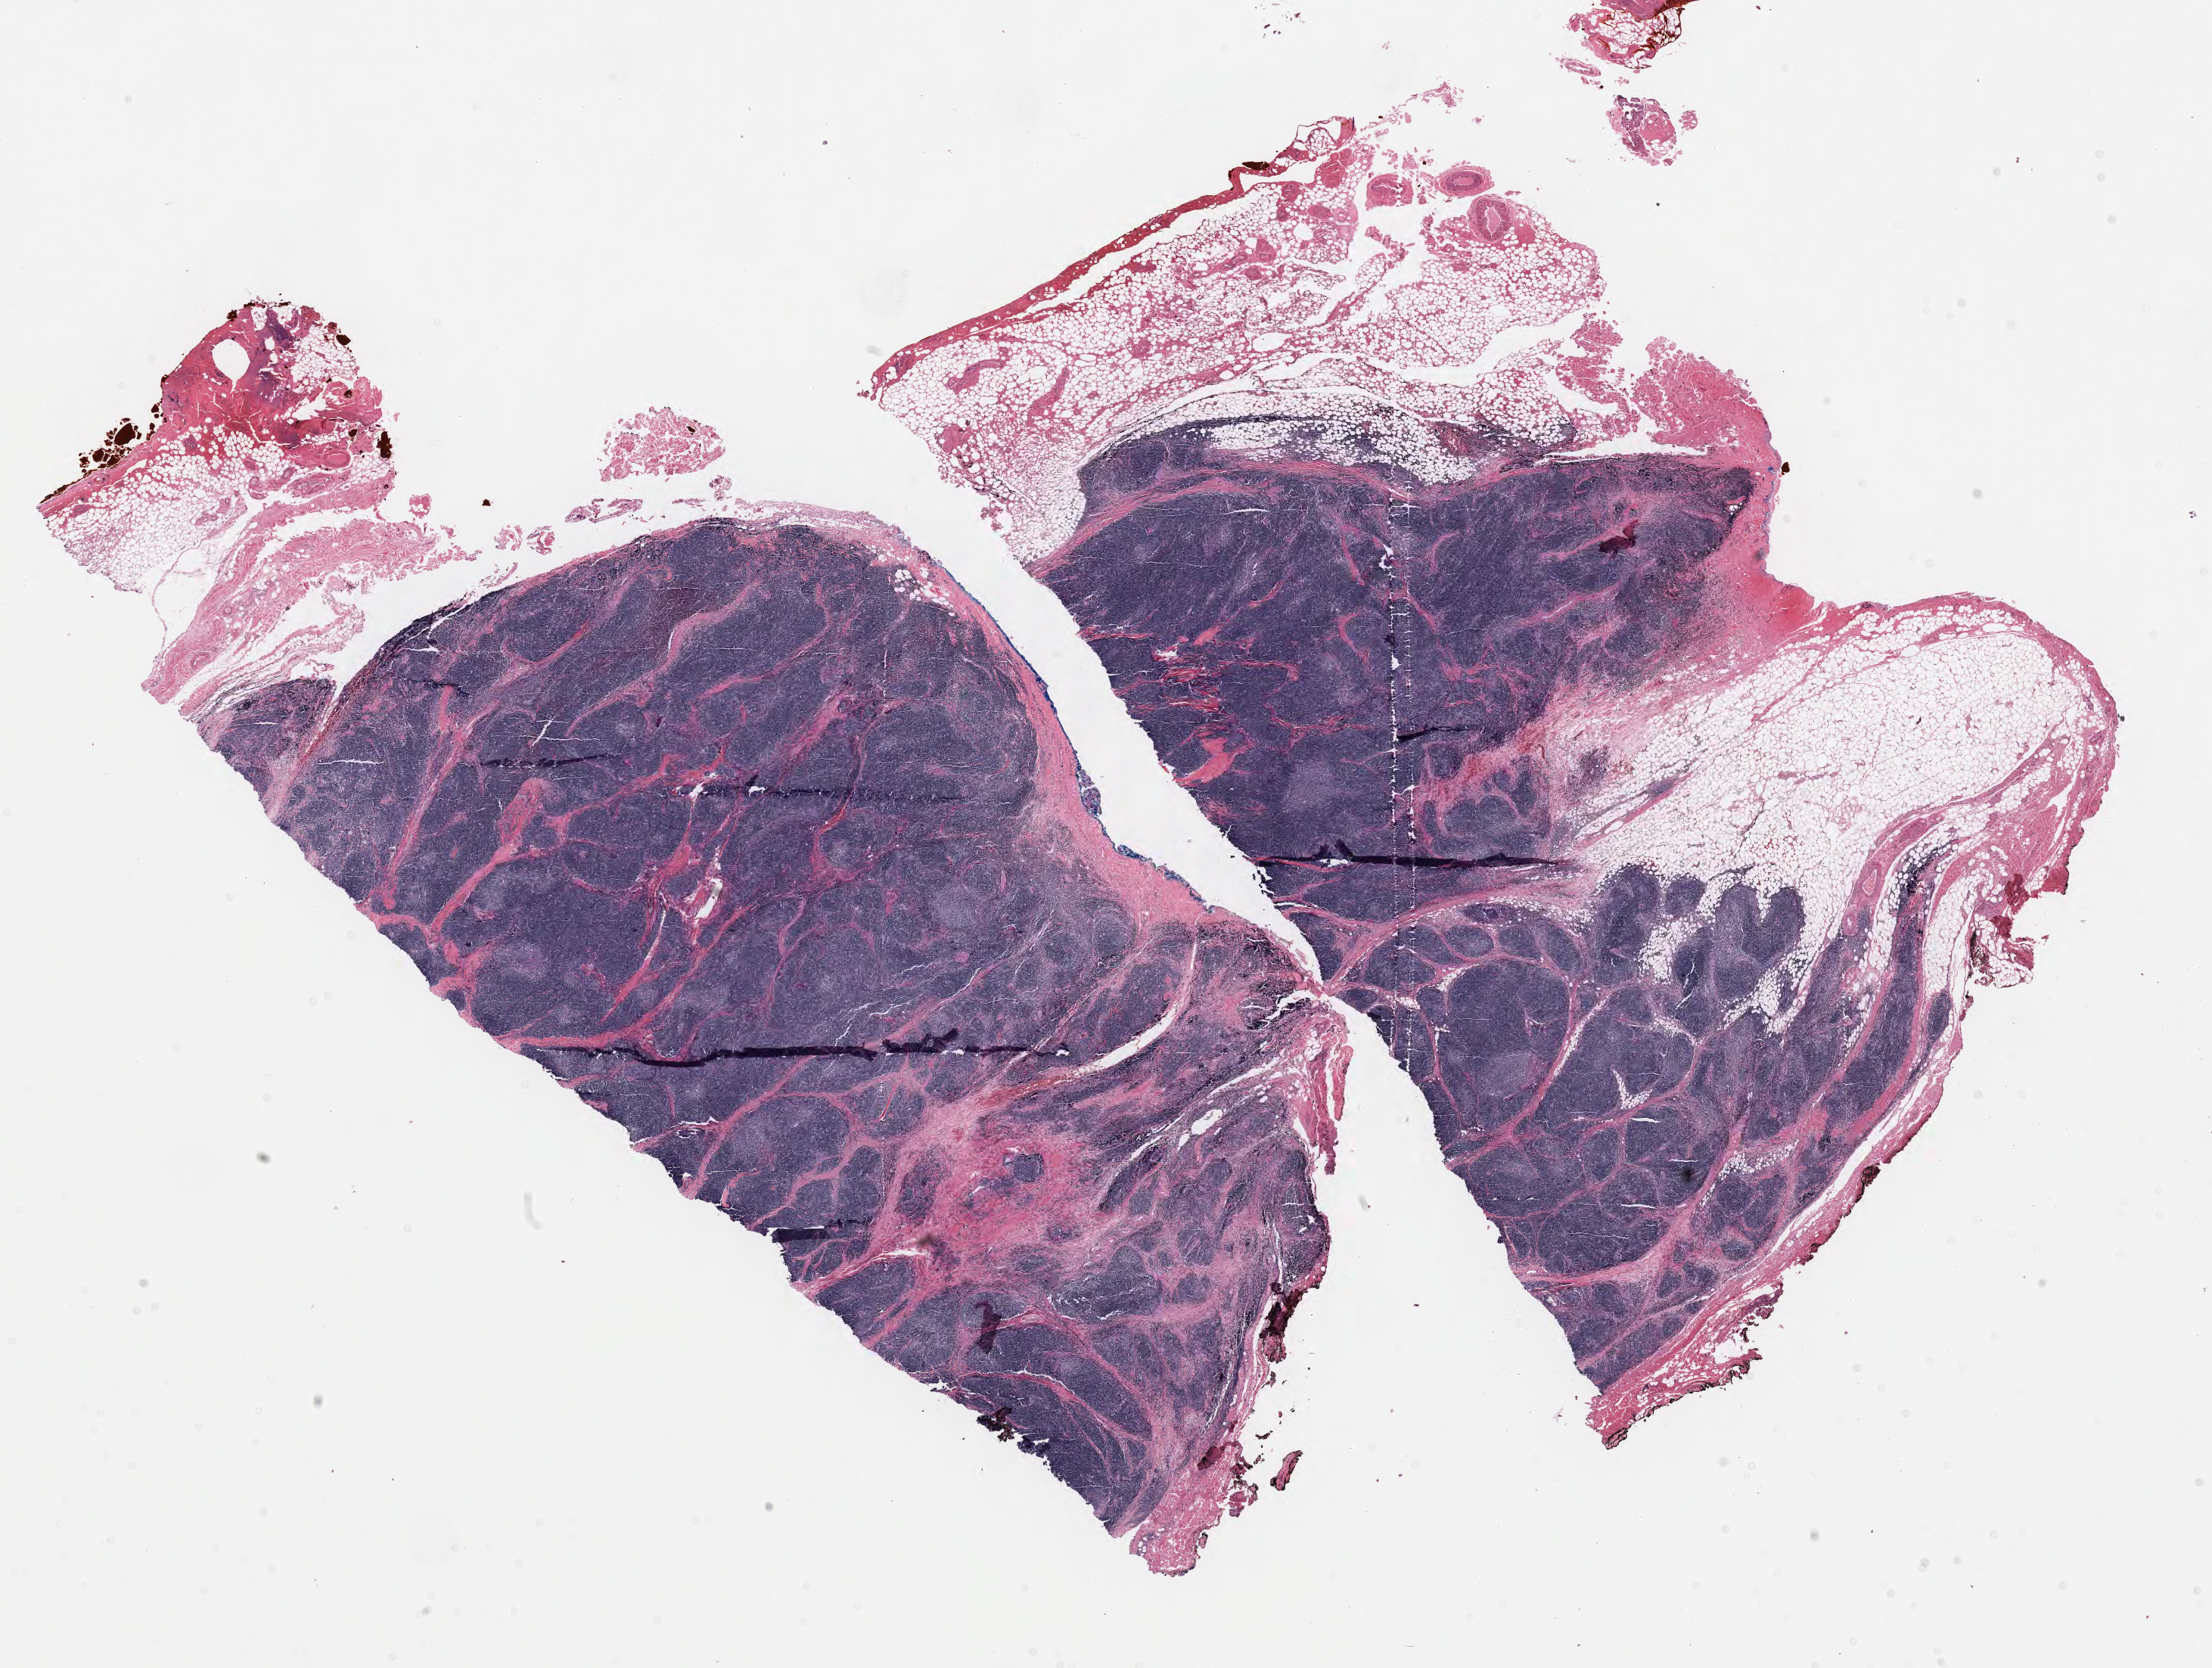
Digitized H&E-stained tissue section (whole slide) — low-resolution overview of the scanned area, about 23.2 x 17.5 mm. Formalin-fixed paraffin-embedded (FFPE) diagnostic section. Thymus, primary tumour sample. Patient: female, age at initial diagnosis 57 years.
* diagnosis: Thymoma, type B1, NOS